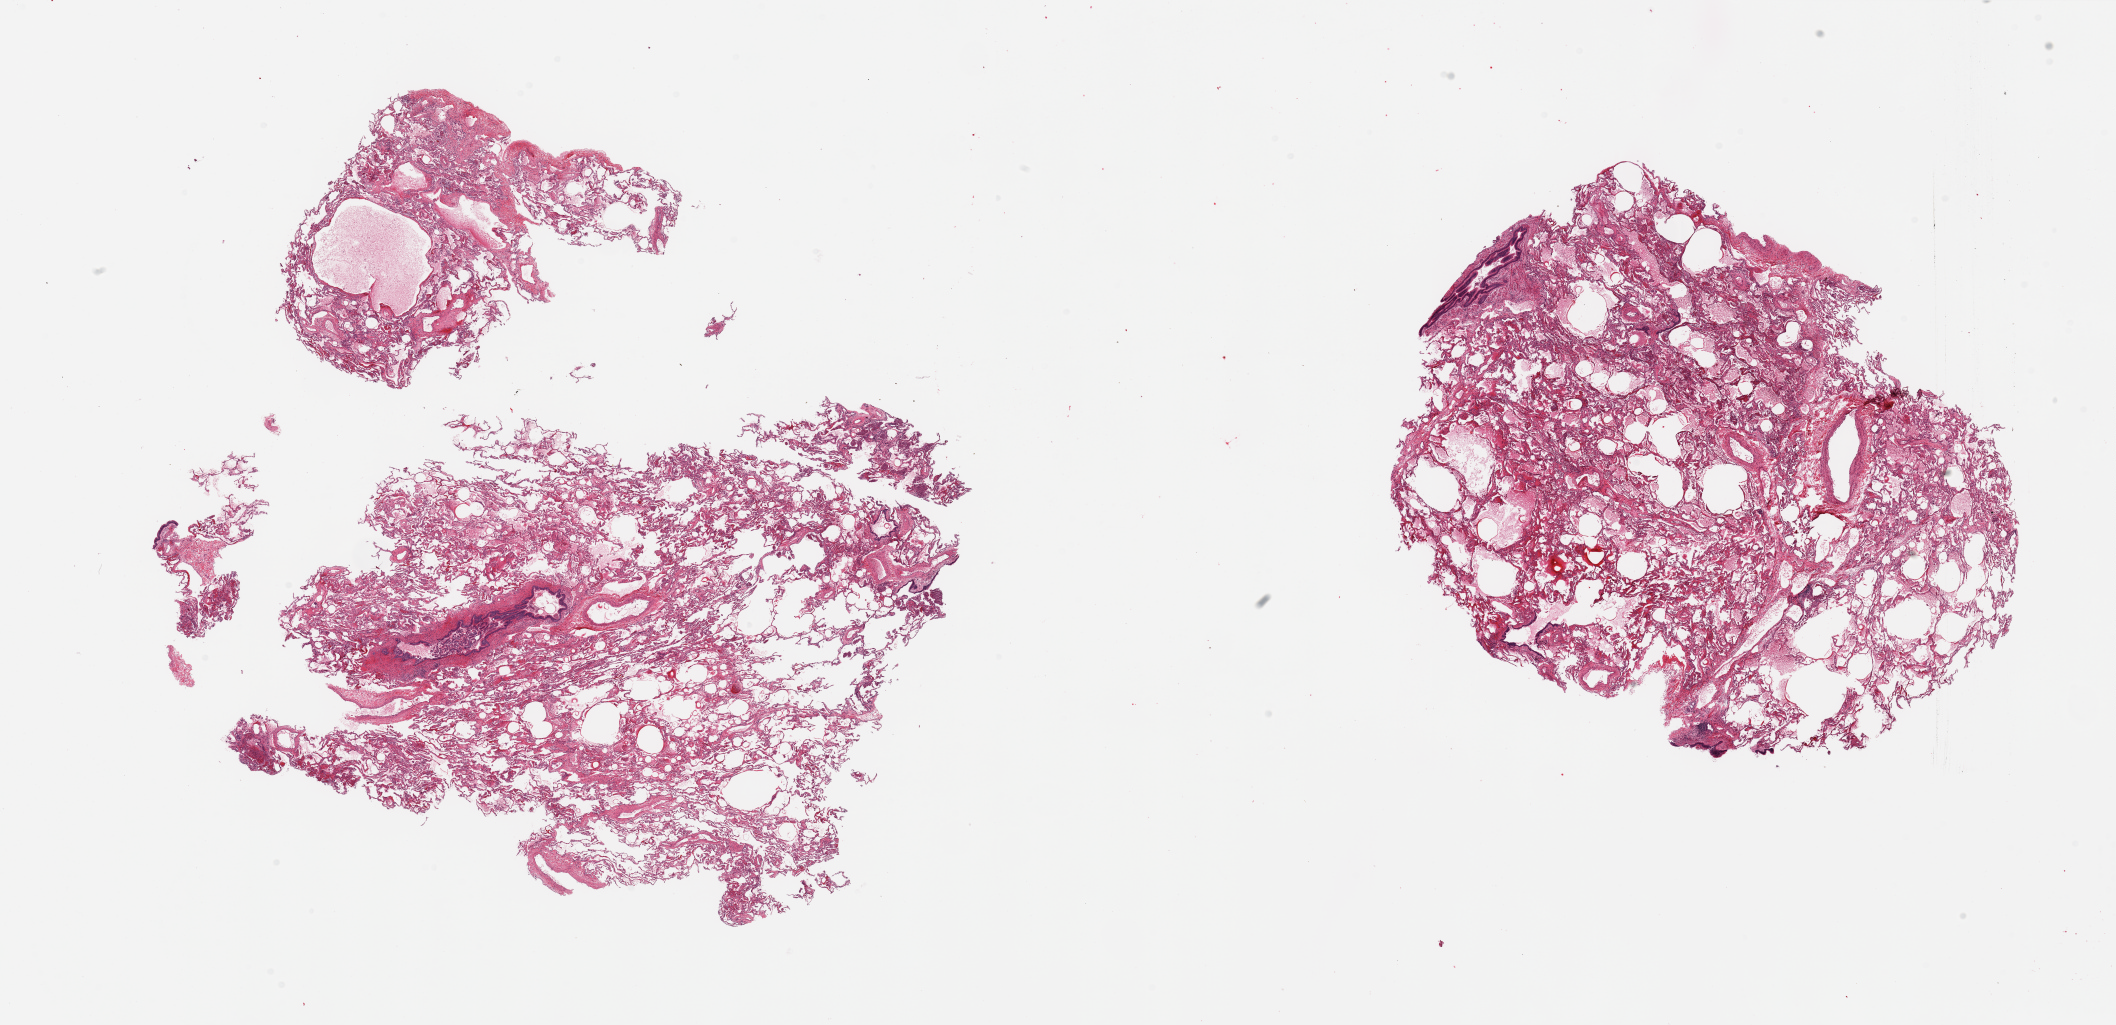
Whole-slide image, hematoxylin and eosin (H&E) stain, brightfield — low-resolution overview of the scanned area, about 33.5 x 16.2 mm (acquisition: 20x scan); PAXgene-fixed, paraffin-embedded tissue; sampled site (target tissue): lung; tissue donor sample. Donor sex: female.
- reviewer comment on this tissue sample: 2 pieces, emphysematous changes, acute bronchitis/pneumonitis, focal, mild